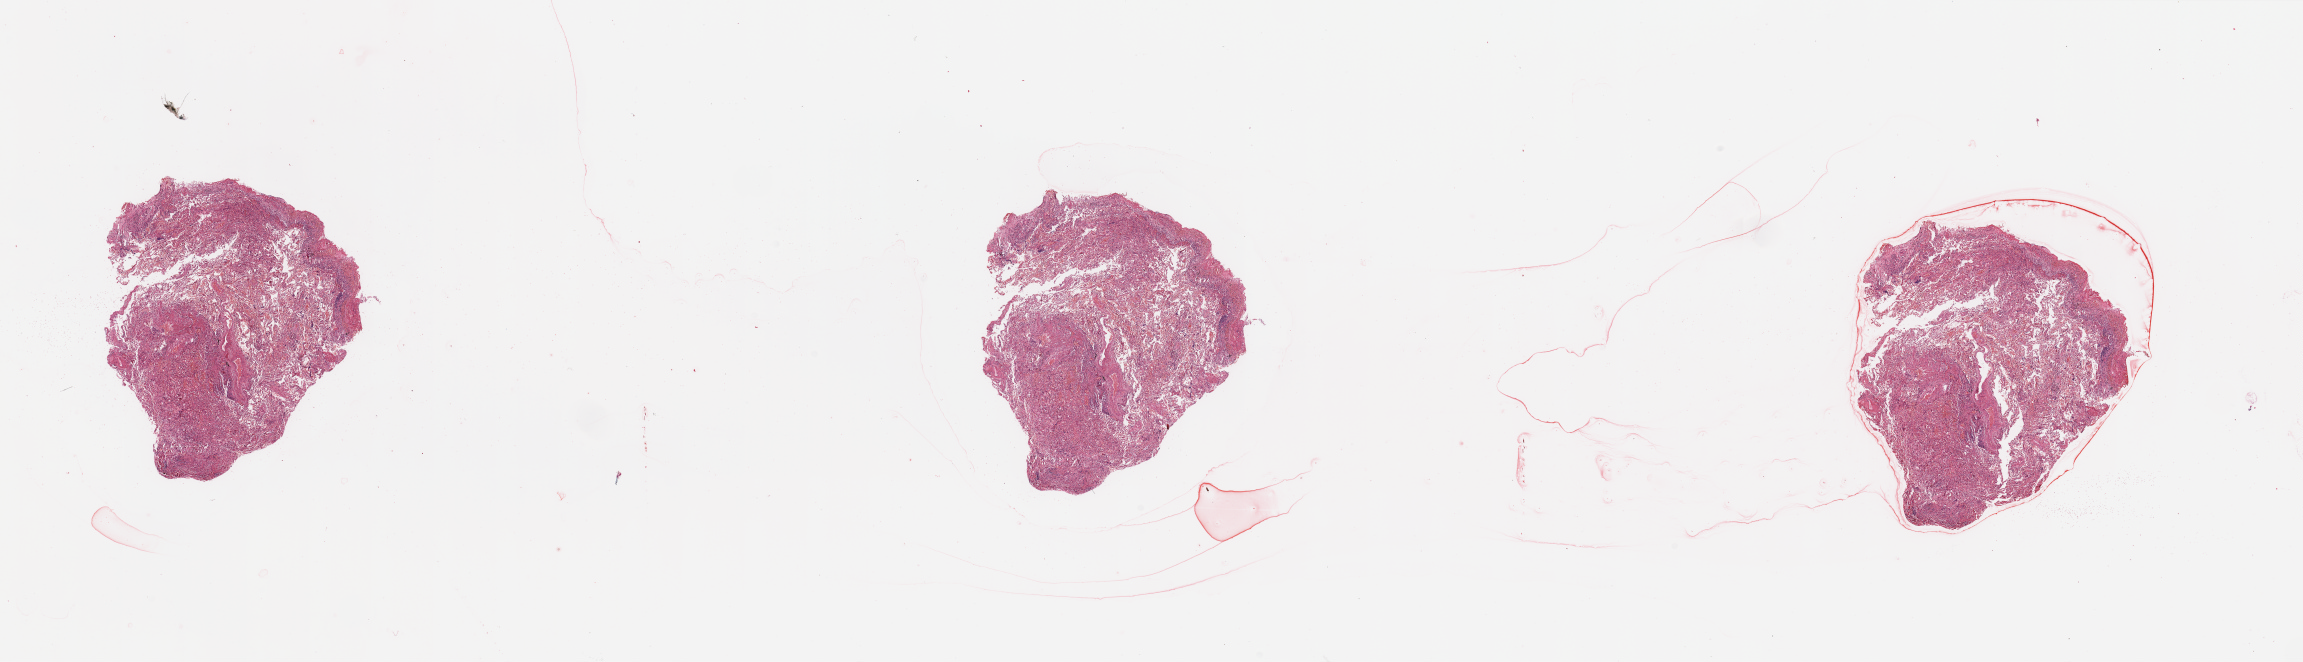
Whole-slide histology image, H&E-stained, low-resolution overview of the scanned area, about 36.4 x 10.5 mm, normal (non-tumour) tissue sample, sampled site: lung. Patient: male, age 73 years.
This section: normal (non-tumour) tissue from the same patient. Patient diagnosis: Squamous cell carcinoma, NOS.